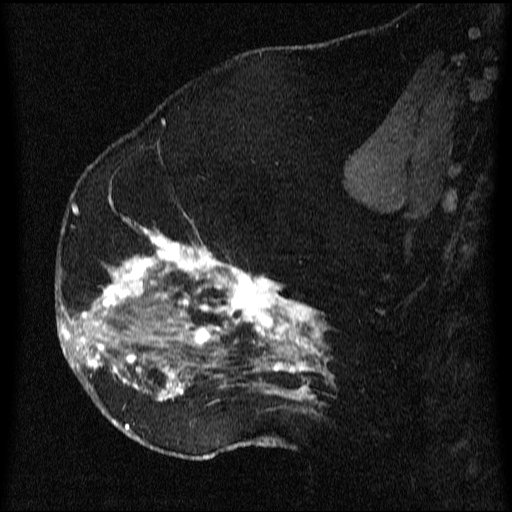
Breast MRI (dynamic contrast-enhanced), one sagittal slice; position 37 of 64 along the scan axis; dynamic contrast-enhanced series, image 2 of 3 at this slice position (ordered by acquisition); 1.5 T; TE 4.2 ms, TR 9.1 ms; 2.2 mm slice thickness; 512 × 512 image matrix. Female patient, age 52 years.
Outlined on this slice (semi-automatically segmented with operator editing):
- analysis volume of interest (the breast-tissue region the enhancement analysis was run in; not a lesion): box from (x=61, y=203) to (x=347, y=438) px
- tumour enhancement mask (voxels above the 70 % enhancement threshold inside the analysis volume of interest): (x=61, y=204)–(x=334, y=432)